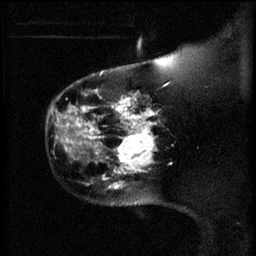
Breast MRI (dynamic contrast-enhanced), one sagittal slice. Position 48 of 60 along the scan axis. 3 images stored at this slice position (order not interpretable as contrast timing). 1.5 T. TE 4.2 ms, TR 11 ms. 2 mm slice thickness. 256 × 256 image matrix, field of view 180 × 180 mm. Patient: female, 44 years.
Outlined on this slice (semi-automatically segmented with operator editing):
- analysis volume of interest (the breast-tissue region the enhancement analysis was run in; not a lesion): box from (x=110, y=124) to (x=159, y=175) px
- tumour enhancement mask (voxels above the 70 % enhancement threshold inside the analysis volume of interest): (x=116, y=124)–(x=155, y=175)